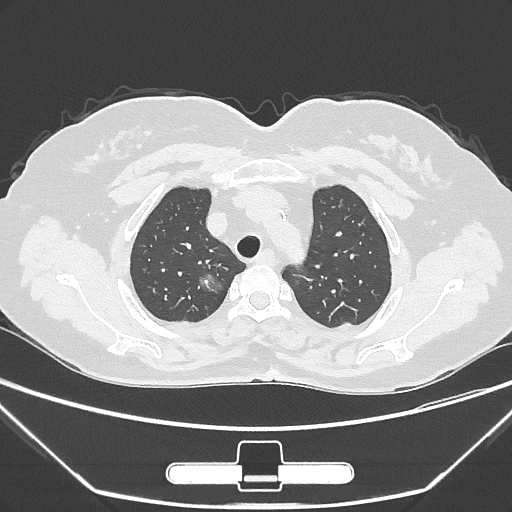
Chest CT, one axial slice. Position 228 of 275 along the scan axis. Reconstruction kernel IMR1,SharpPlus. Lung window (W 1500 / L -600 HU). 512 × 512 image matrix, field of view 356 × 356 mm. Female patient, age 63 years. Case-level facts recorded for this patient, not image findings: clinical TNM (as recorded): T1a N0 M0; histopathological grade: G1.
Annotated regions visible in this slice (bounding box drawn by a radiologist):
- lung tumour (recorded histology: adenocarcinoma): bounding box <187,268,230,300> (left, top, right, bottom; pixels)